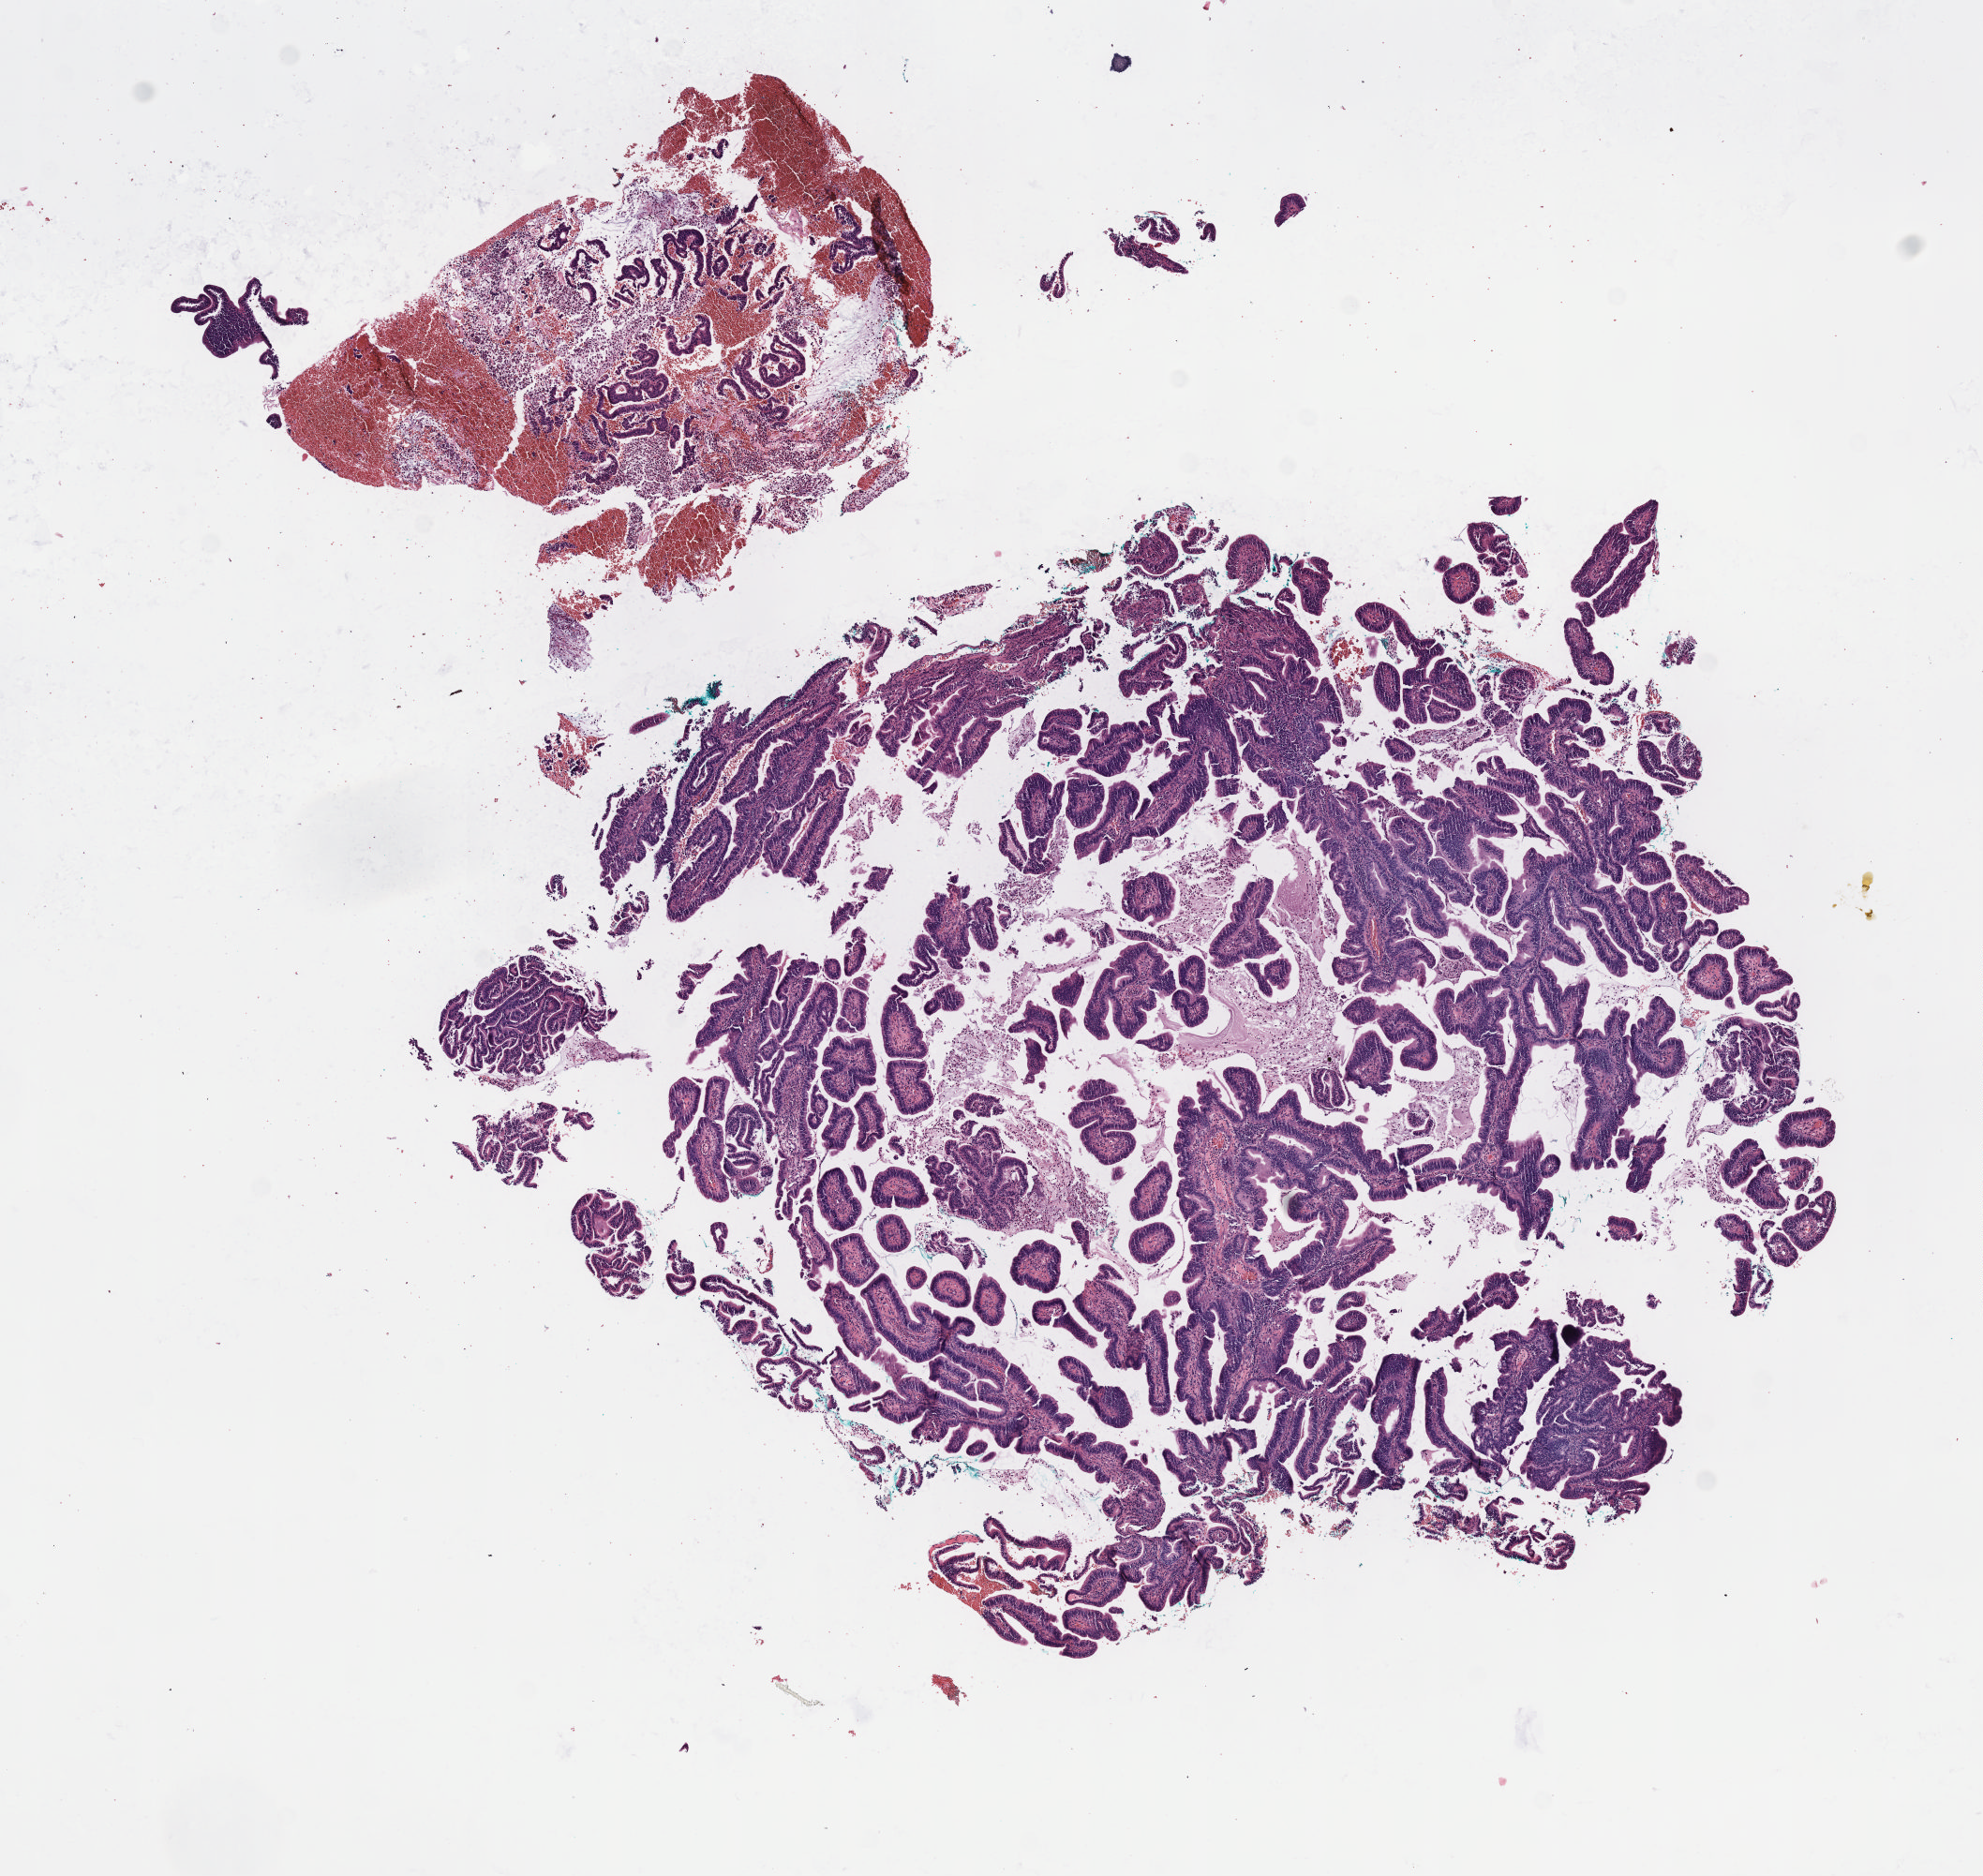
Digitized H&E tissue section (whole slide), a low-resolution overview of the entire scanned area, about 8.6 x 8.1 mm. FFPE section. Primary tumour sample from the cervix. Female, age 43 years at initial diagnosis. Histologic grade: G2 (moderately differentiated).
- diagnosis: Mucinous adenocarcinoma, endocervical type
- FIGO stage: IIB